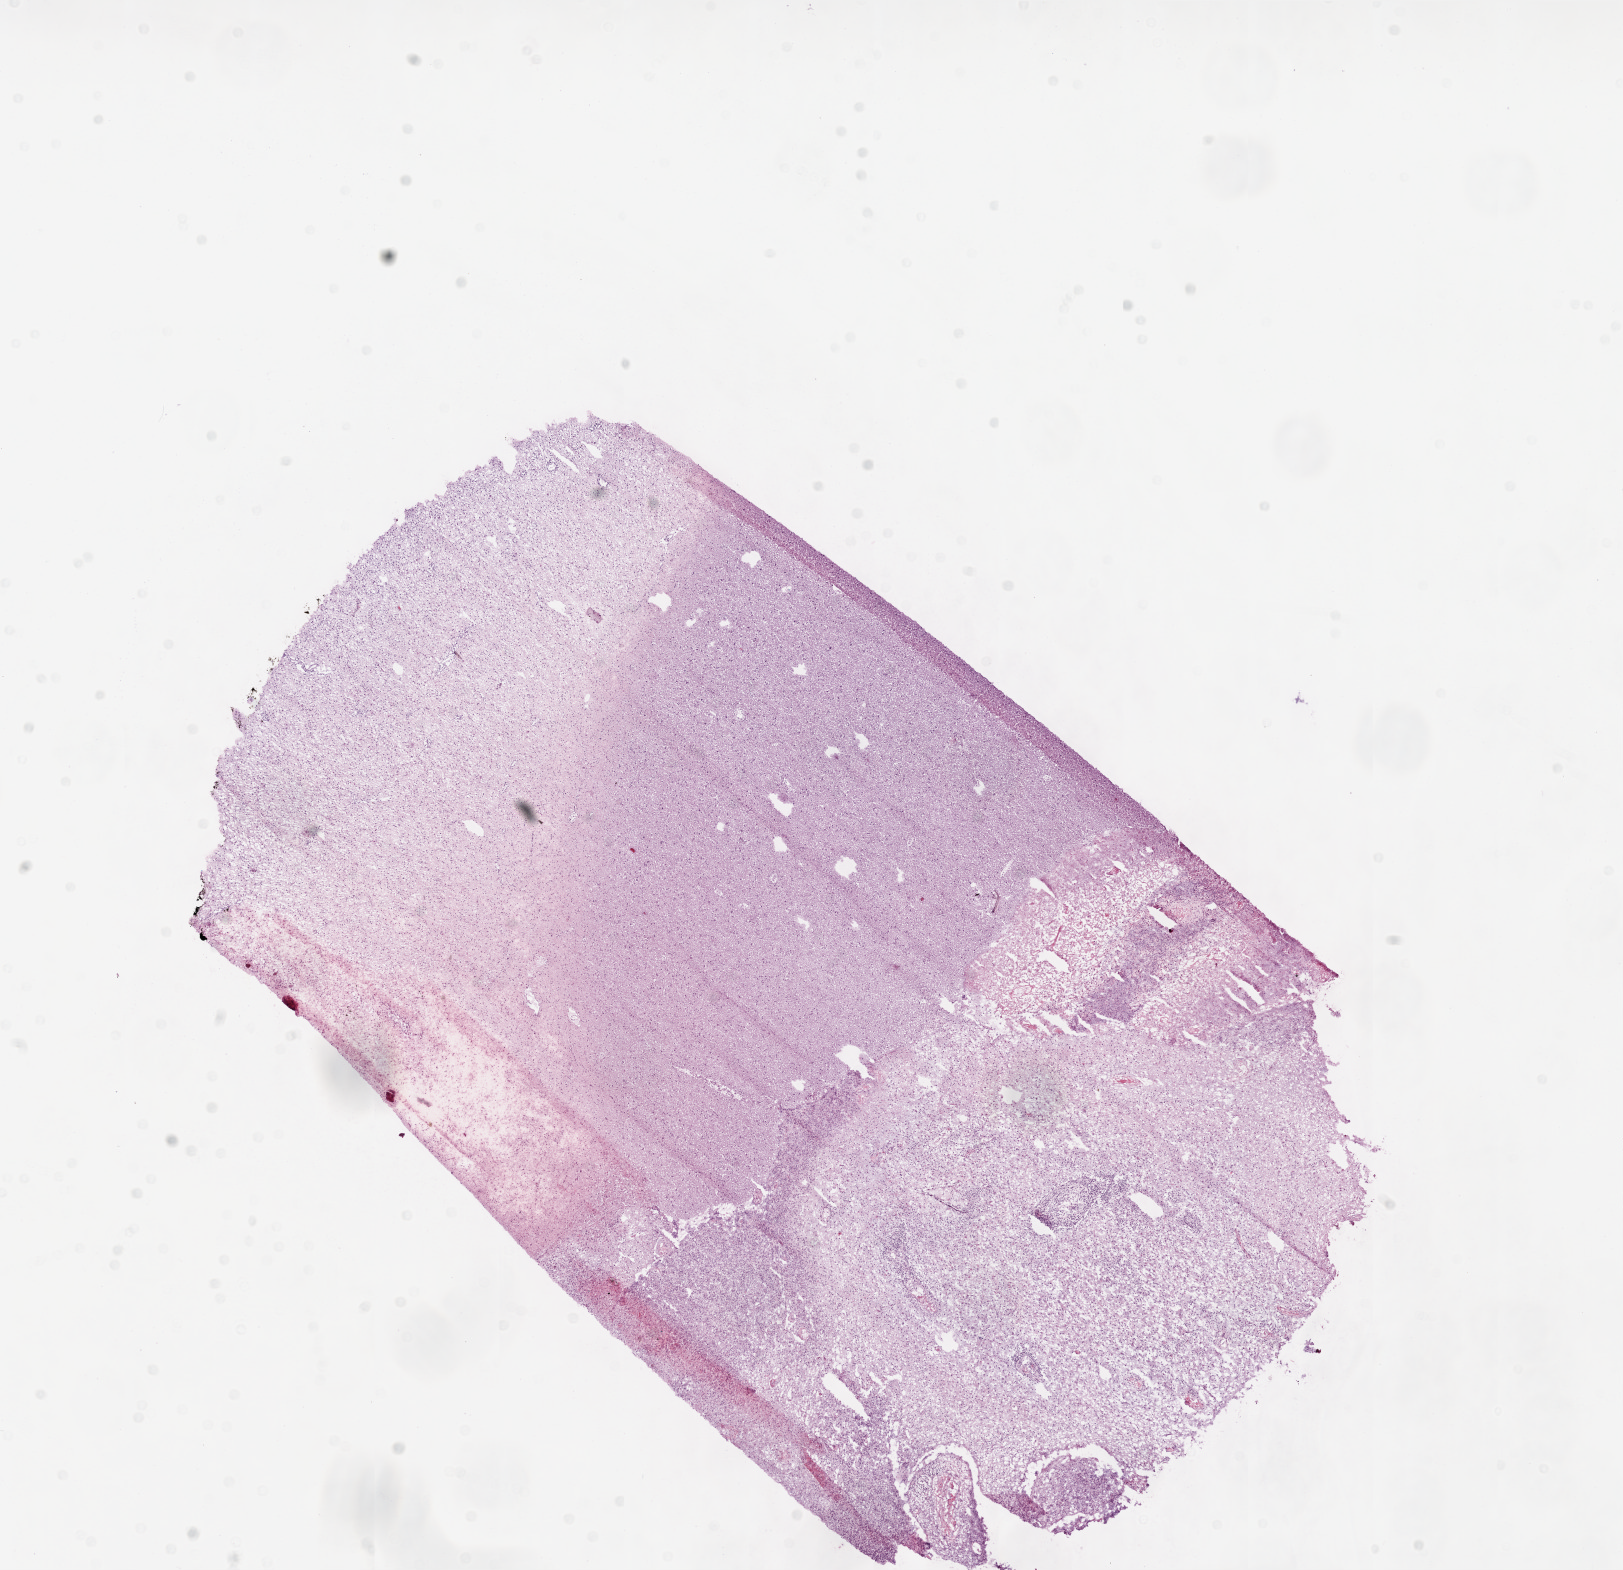
H&E-stained whole-slide image, shown as a low-resolution overview of the whole scanned area (about 13.0 x 12.6 mm); frozen section; brain, primary tumour sample. Male, age 49 years at initial diagnosis. Slide review estimates, as recorded: tumour cells 90%, tumour nuclei 100%, normal cells 10%, stromal cells 0%, necrosis 0%.
Histologic diagnosis: Glioblastoma.